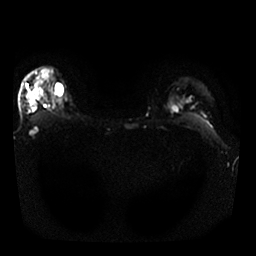
Breast MRI, one axial slice. Position 22 of 30 along the scan axis. Diffusion-weighted series; image 2 of 4 stored at this slice position (different b-values; order by instance number). 1.5 T. 4 mm slice thickness. 256 × 256 image matrix. Female patient.
Structures marked on this image (outlined manually by an expert reader):
- tumour on diffusion-weighted imaging: box from (x=40, y=70) to (x=51, y=80) px